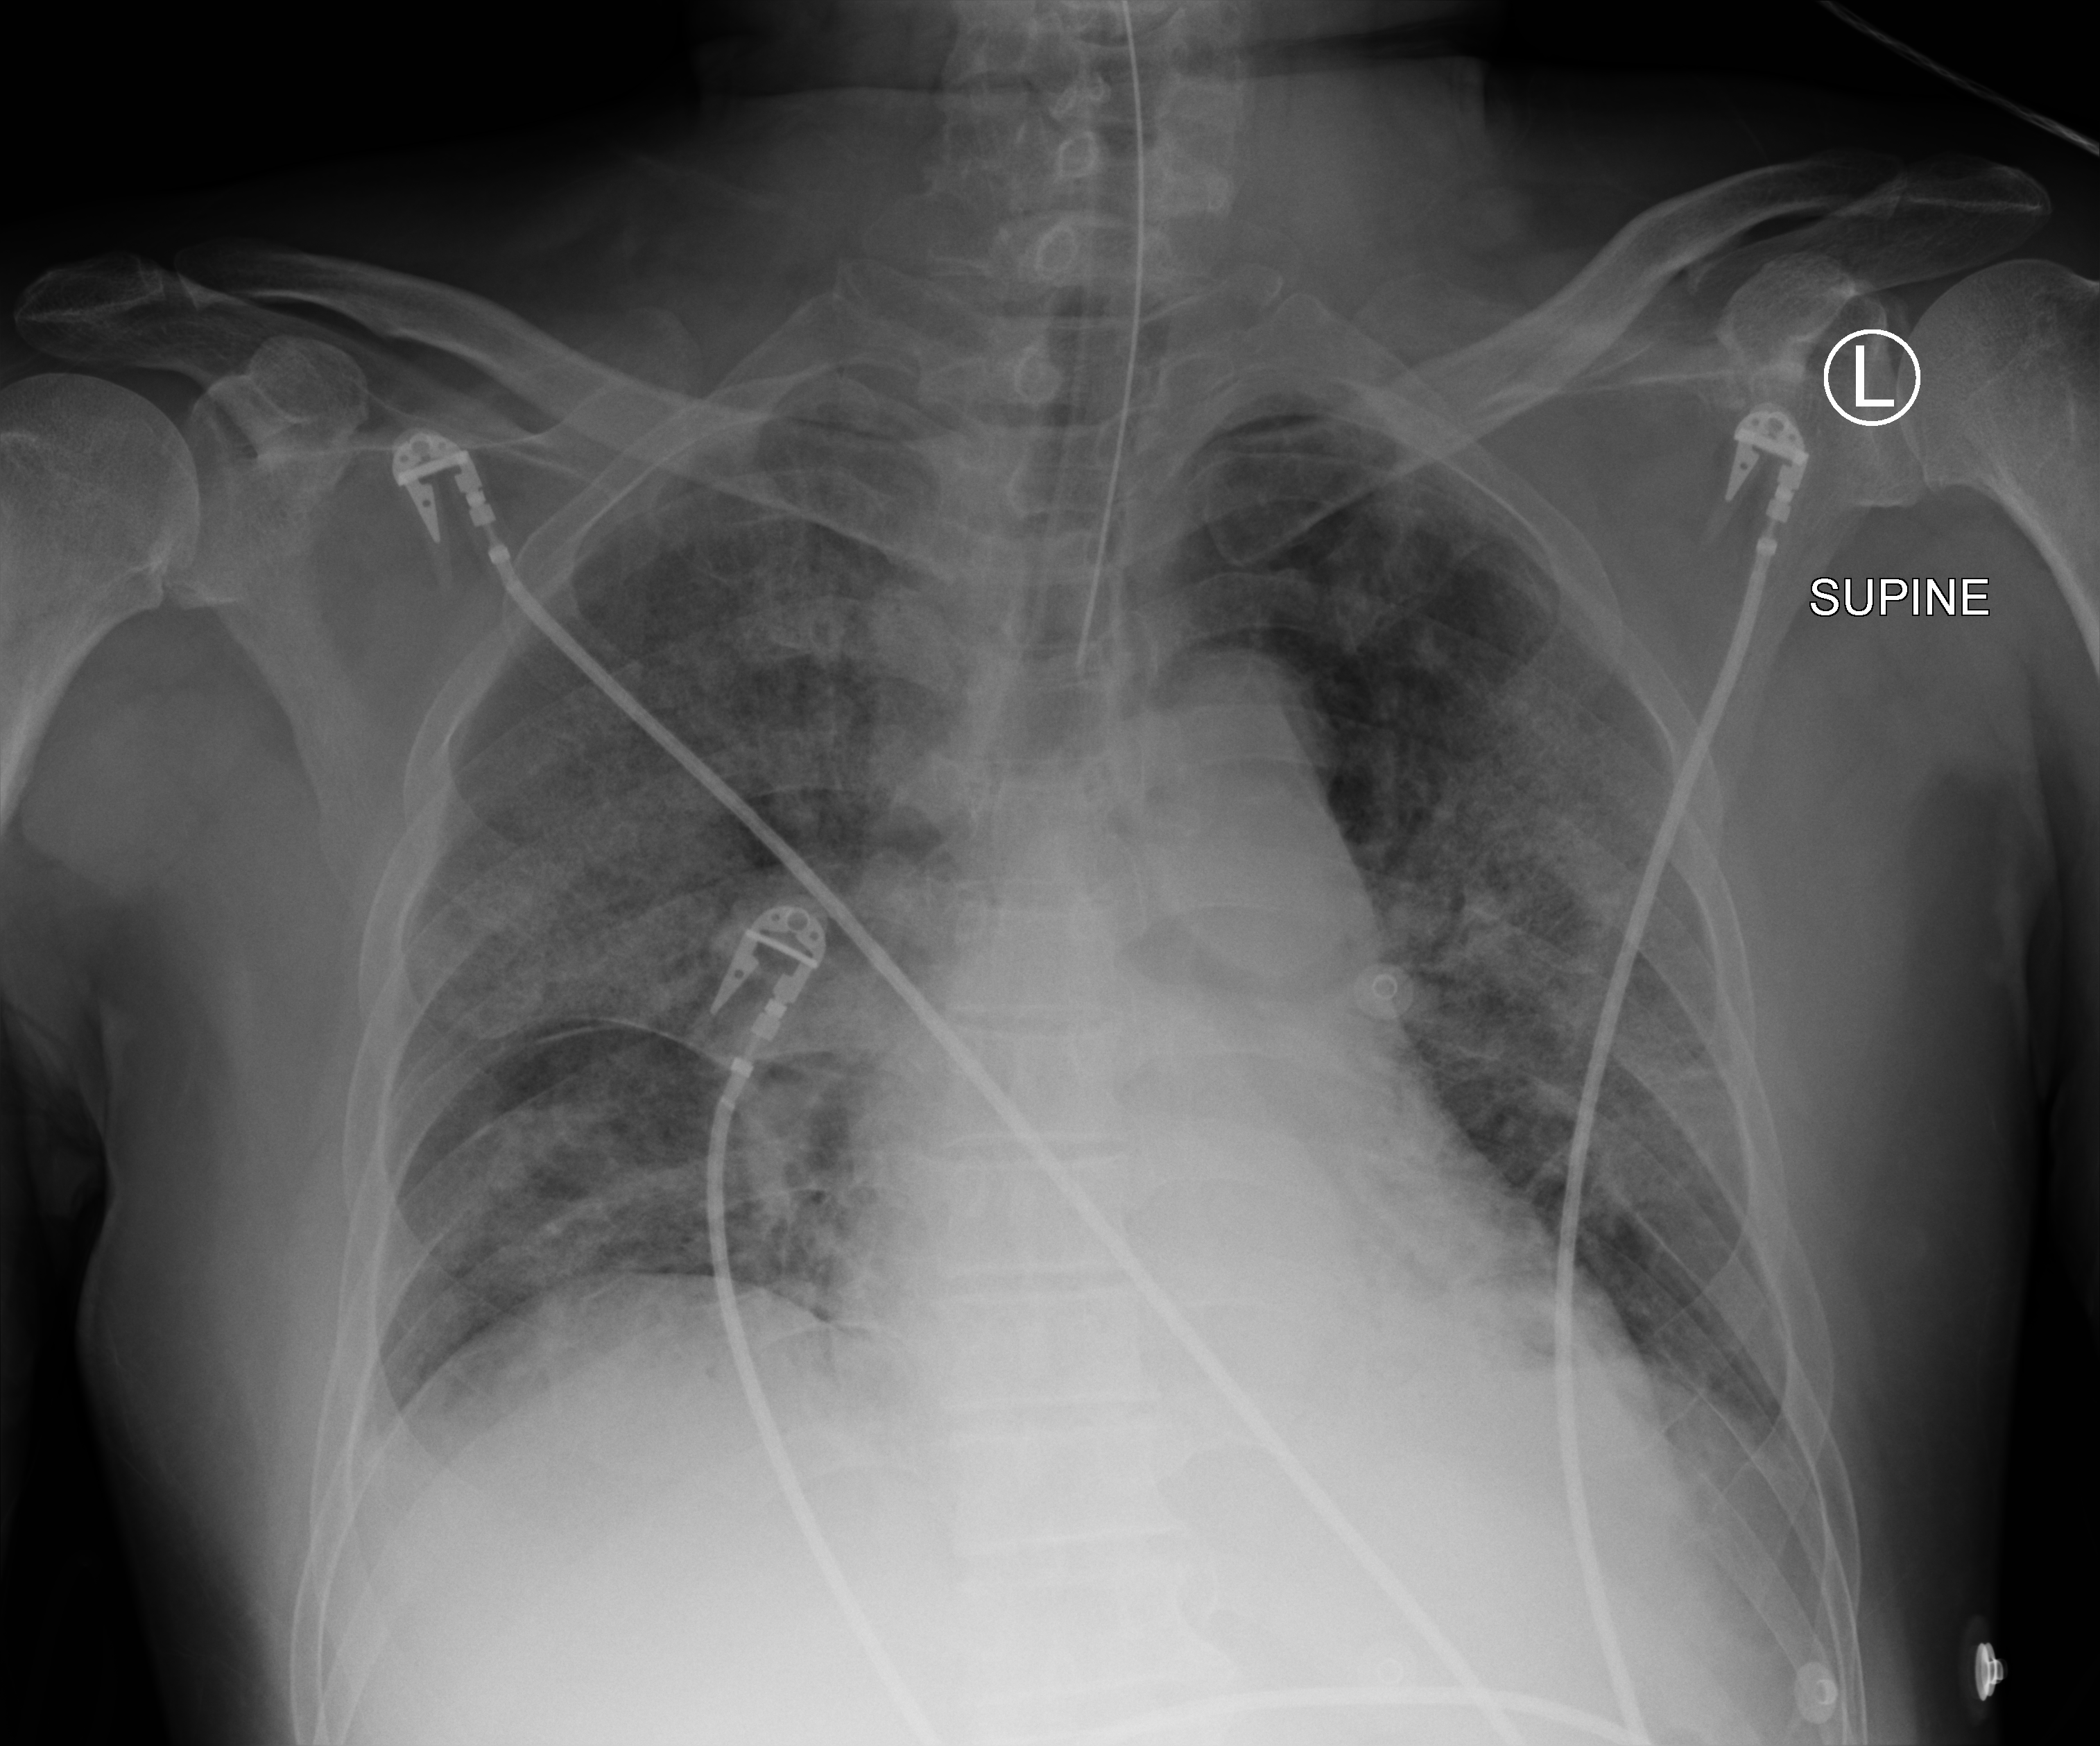
Chest X-ray (portable); anteroposterior (AP) projection. Male patient hospitalised with COVID-19, age 60–74 years.
Admission-level facts for this patient (not findings on this image; timing relative to this image not recorded): admitted to intensive care during this hospital stay: yes; mechanically ventilated during this hospital stay: yes.